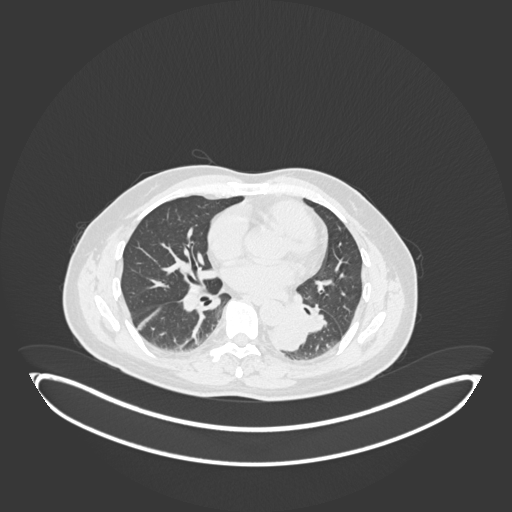
Chest CT, one axial slice. Position 88 of 258 along the scan axis. Reconstruction kernel B30f. 120 kVp. Lung window (W 1500 / L -600 HU). 1 mm slice thickness. 512 × 512 image matrix, field of view 500 × 500 mm. Patient: male, 54 years. From the clinical record (not read from this slice): clinical TNM (as recorded): T3 N0 M0.
Annotated regions visible in this slice (rectangle marked by the reading radiologist):
- lung tumour (recorded histology: squamous cell carcinoma): bounding box <271,300,309,353> (left, top, right, bottom; pixels)